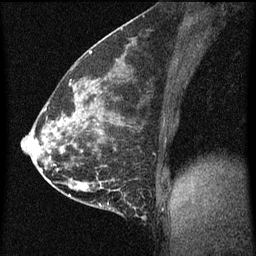
Breast MRI (dynamic contrast-enhanced), one sagittal slice; dynamic contrast-enhanced series, image 2 of 3 at this slice position (ordered by acquisition); 1.5 T; TE 4.2 ms, TR 8 ms; 256 × 256 image matrix, field of view 180 × 180 mm. Patient: female, 35 years.
Structures marked on this image (semi-automatic segmentation, software-assisted and operator-edited):
- analysis volume of interest (the breast-tissue region the enhancement analysis was run in; not a lesion): bounding box <110,178,148,219> (left, top, right, bottom; pixels)
- tumour enhancement mask (voxels above the 70 % enhancement threshold inside the analysis volume of interest): <135,208,137,211>